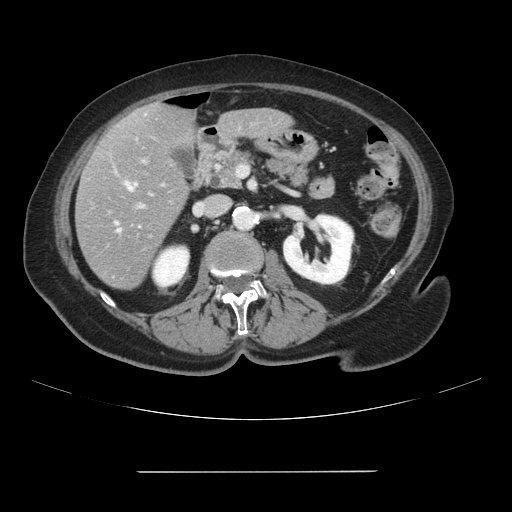
Contrast-enhanced abdominal CT, one axial slice. Position 38 of 111 along the scan axis. Intravenous contrast given. Soft-tissue window (W 400 / L 40 HU). 2.5 mm slice thickness. 512 × 512 image matrix, field of view 400 × 400 mm. Female patient, age 74 years. From the clinical record (not read from this slice): diagnosis: colorectal cancer liver metastases, imaged before liver resection; multiple liver metastases: yes; largest metastasis: 1.1 cm; disease in both lobes: yes.
Annotated regions visible in this slice (manually delineated by an expert):
- hepatic veins: box from (x=127, y=184) to (x=133, y=190) px
- liver: (x=76, y=103)–(x=293, y=289)
- planned liver remnant (the part of the liver to remain after resection): (x=140, y=103)–(x=292, y=149)